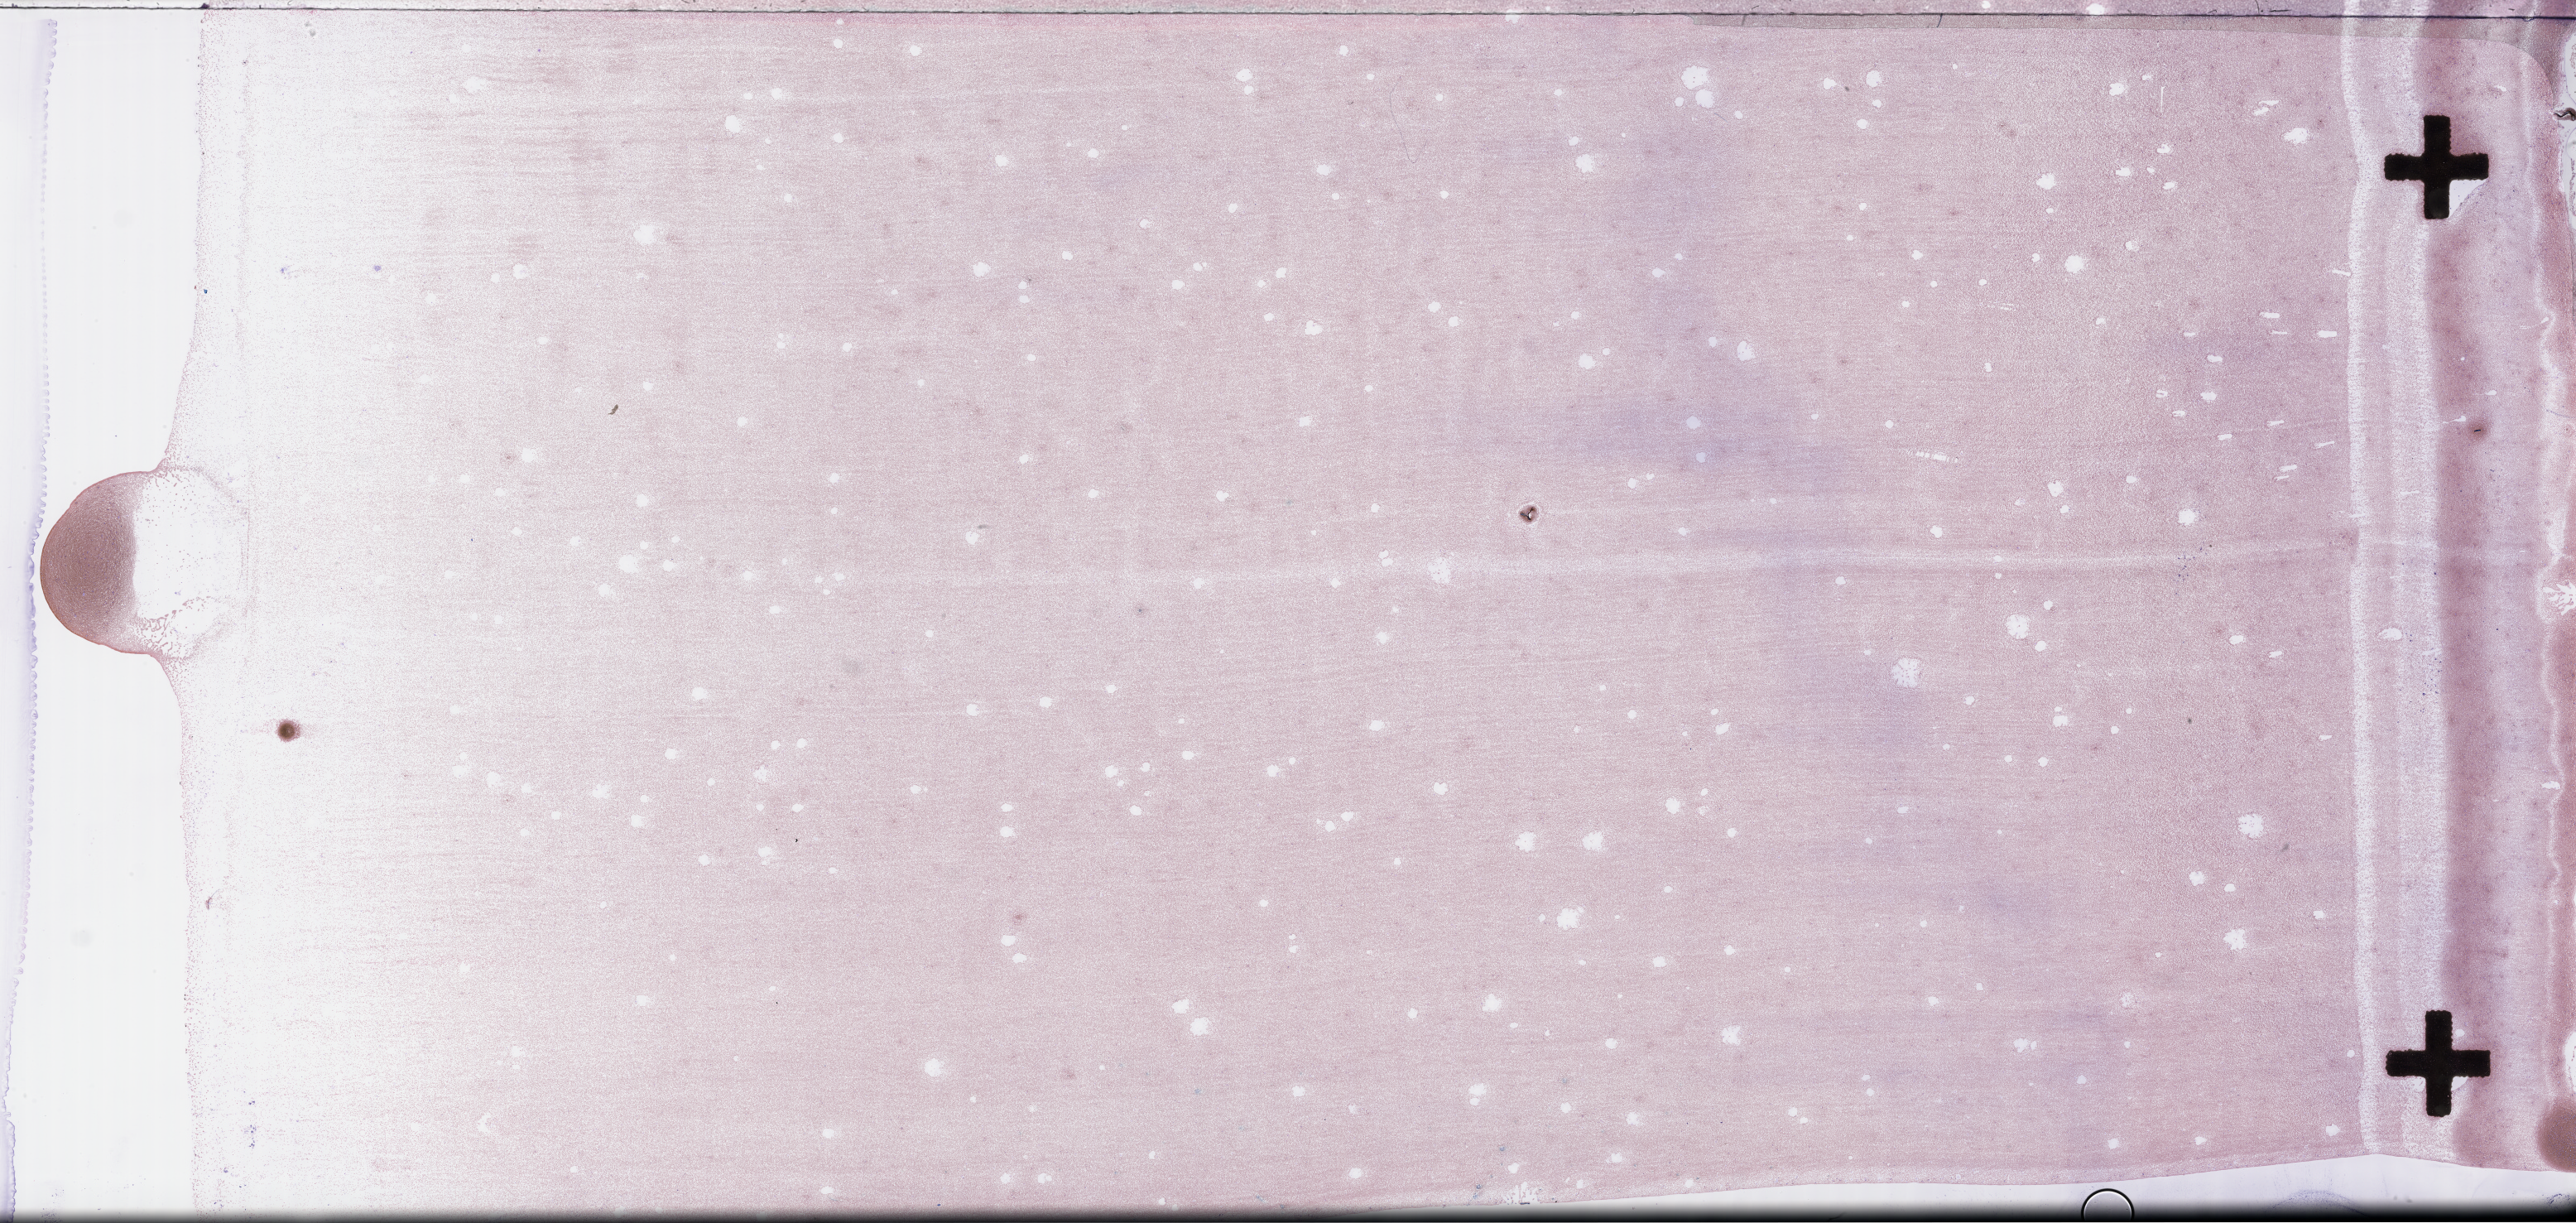
Wright–Giemsa-stained bone marrow smear, whole-slide image, low-resolution overview of the scanned area, about 50.3 x 23.9 mm, collected on treatment. Patient: male.
Patient diagnosis: Plasma Cell Myeloma.